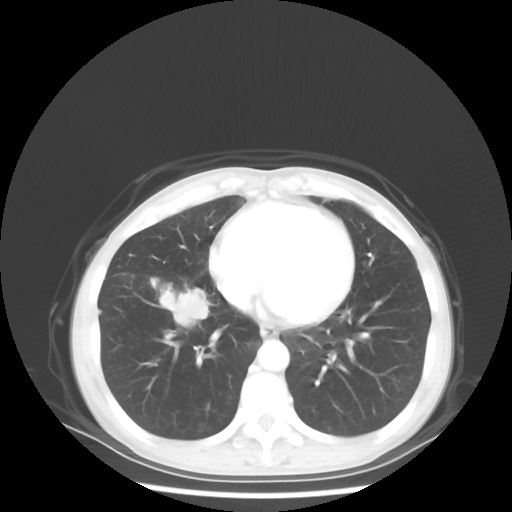
Chest CT, one axial slice. Position 19 of 56 along the scan axis. Reconstruction kernel STANDARD. Lung window (W 1500 / L -600 HU). 5 mm slice thickness. 512 × 512 image matrix, field of view 360 × 360 mm. Female patient, age 57 years. From the clinical record (not read from this slice): clinical TNM (as recorded): T1c N3 M1a; histopathological grade: G3.
Annotated regions visible in this slice (bounding box drawn by a radiologist):
- lung tumour (recorded histology: adenocarcinoma): bounding box [x1, y1, x2, y2] px = [156, 284, 213, 327]